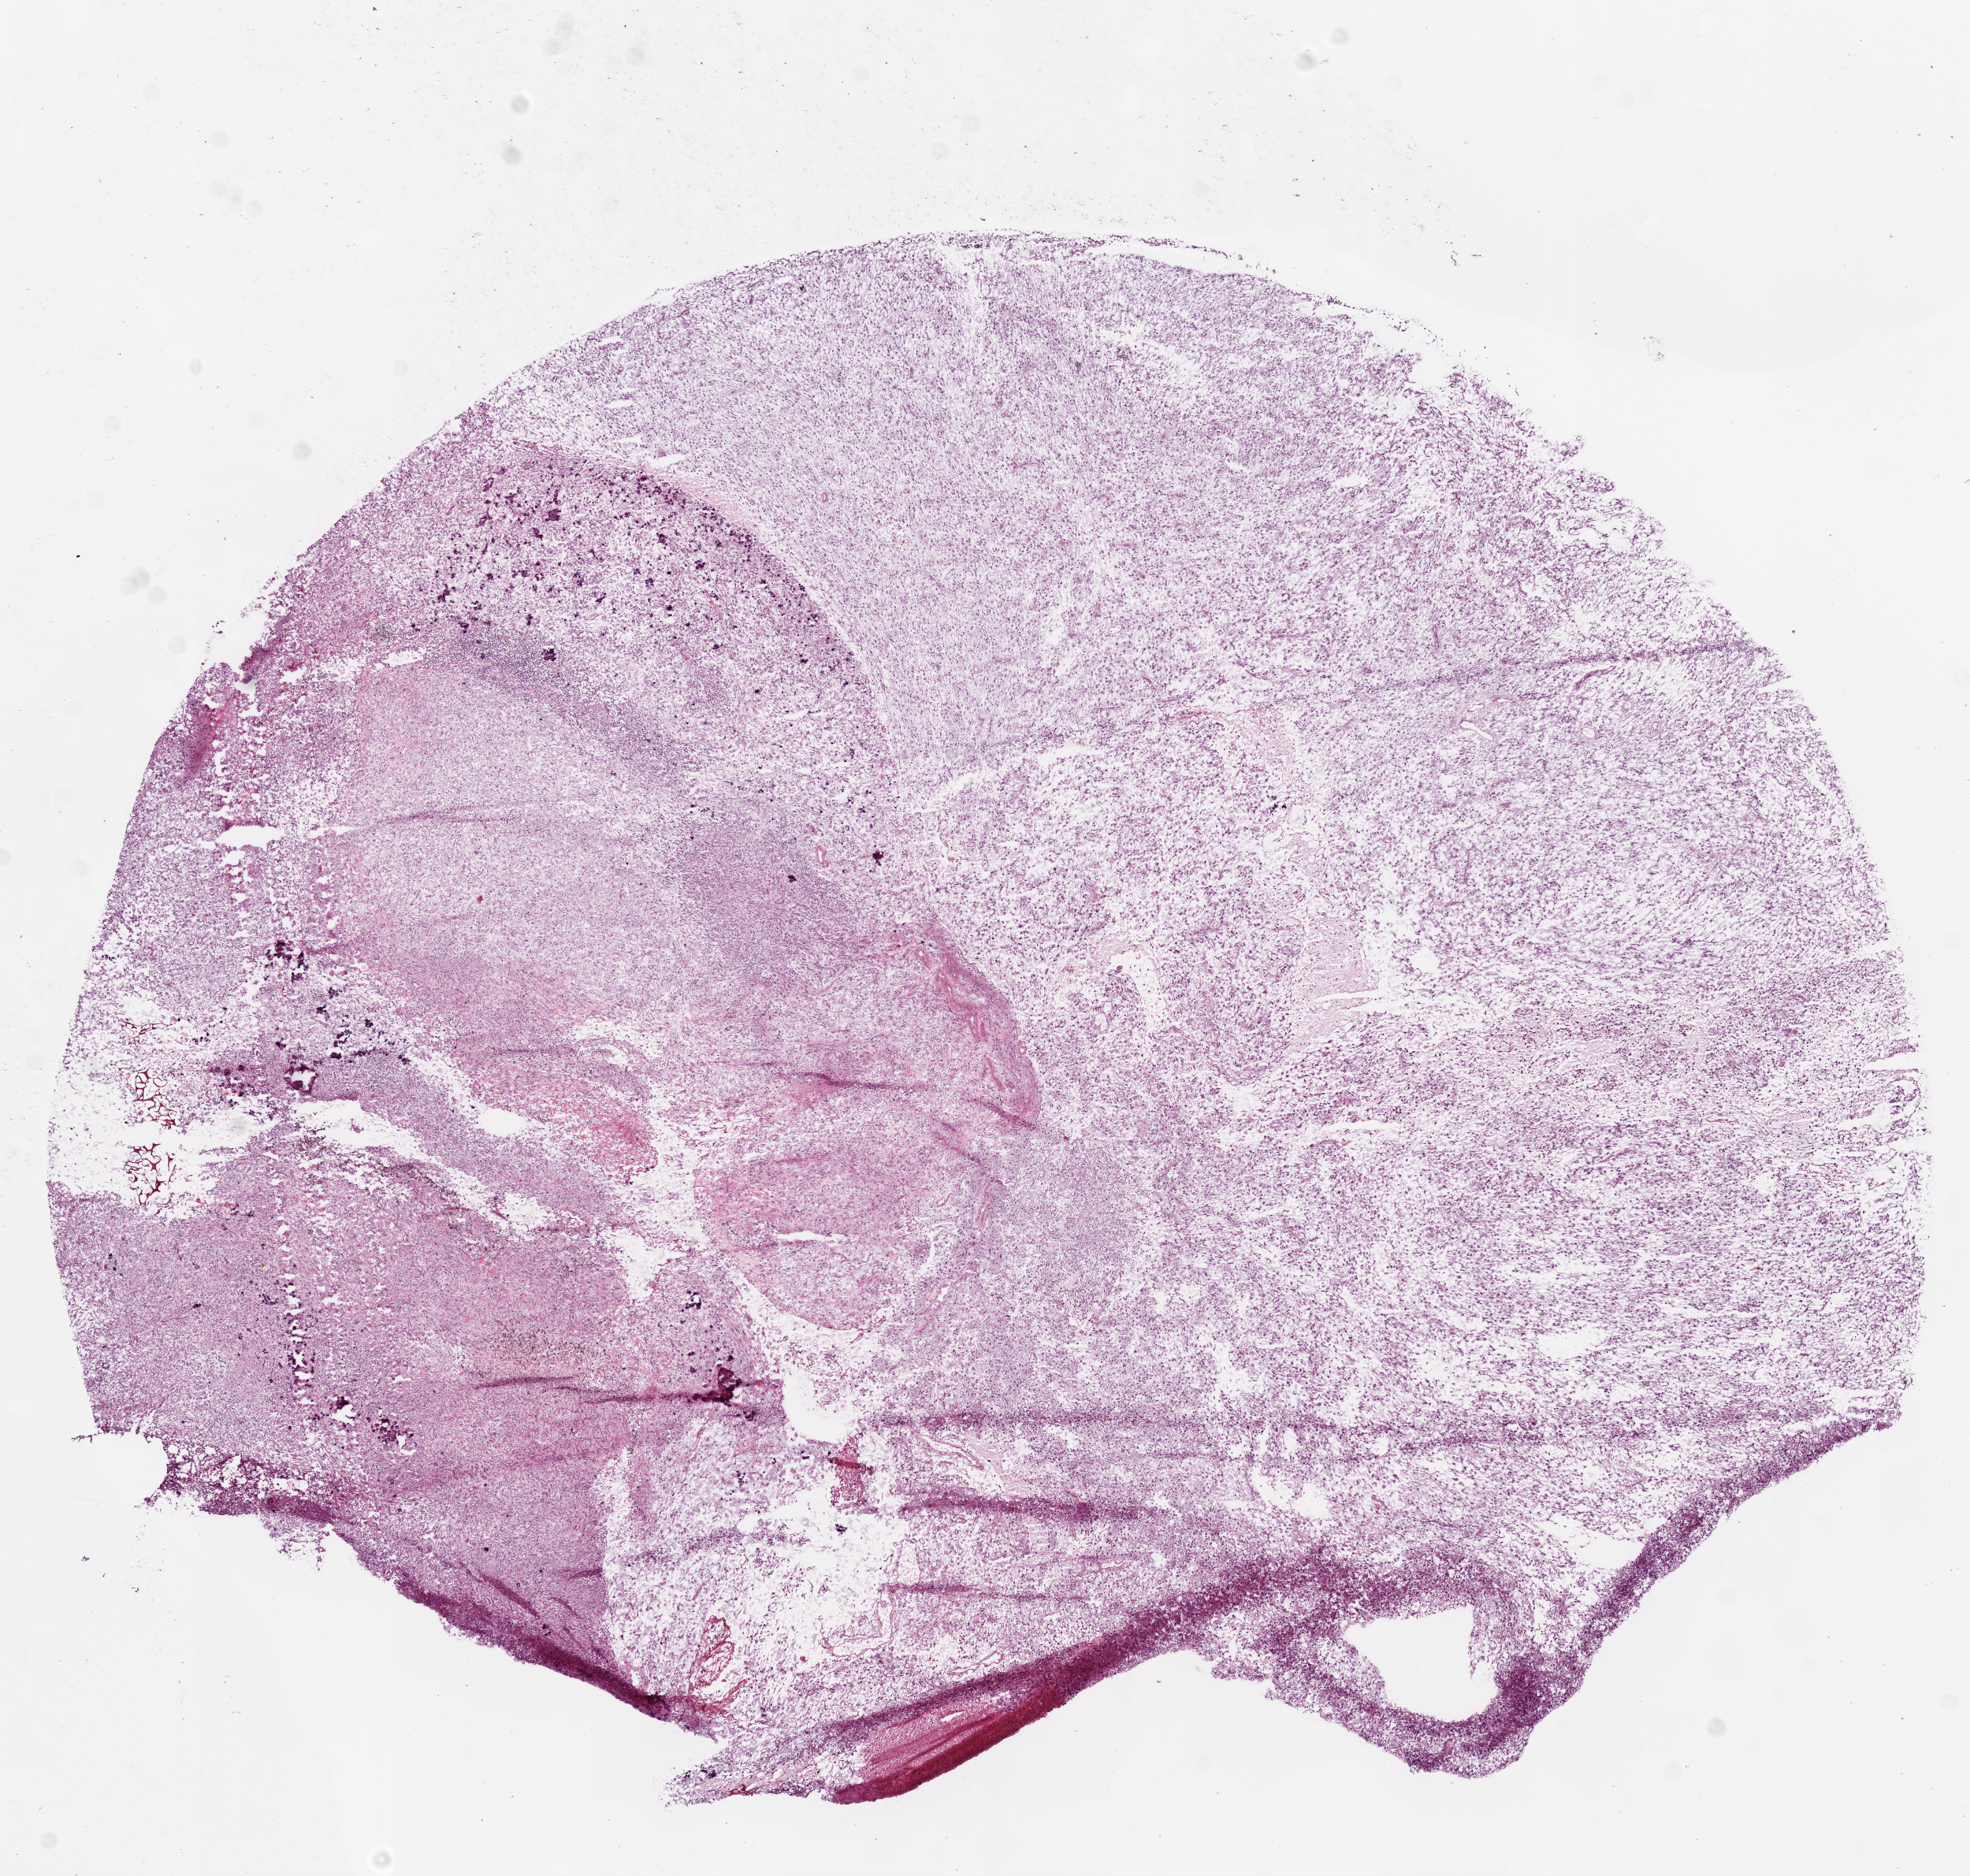
Whole-slide histology image, H&E — whole scanned area (about 10.0 x 9.6 mm, from a 20x scan) shown as a low-resolution overview; frozen section from the bottom of the tissue portion; brain, primary tumour sample. Male patient; age at initial diagnosis 47 years. Slide review estimates, as recorded: tumour cells 70%, tumour nuclei 80%, normal cells 15%, stromal cells 10%, necrosis 5%. Inflammatory infiltration, as recorded: lymphocyte infiltration 50%, monocyte infiltration 50%.
Pathologic diagnosis: Glioblastoma.